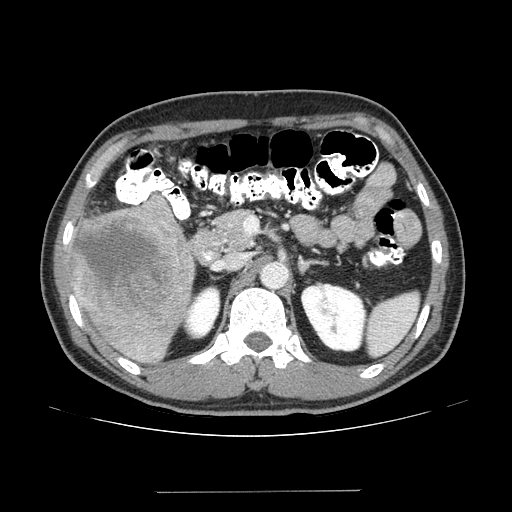
Contrast-enhanced abdominal CT (liver protocol), one axial slice; slice 72 of 131 in the series (ordered by position); reconstruction kernel STANDARD; 100 kVp; one of 2 acquisitions stored at this slice position; soft-tissue window (W 400 / L 40 HU); 512 × 512 image matrix, field of view 380 × 380 mm. Case-level facts recorded for this patient, not image findings: diagnosis: hepatocellular carcinoma (patient treated with transarterial chemoembolisation; whether this scan precedes or follows treatment is not stated here); TNM stage (as recorded): Stage-I; Child-Pugh class: A; tumour differentiation: poorly differentiated; tumour nodularity: uninodular.
Annotated regions visible in this slice (semi-automatic segmentation, software-assisted and operator-edited):
- liver parenchyma outside the tumour (the mass and vessels are separate outlines, so this box may not span the whole liver): box from (x=68, y=199) to (x=194, y=362) px
- mass: (x=72, y=195)–(x=193, y=326)